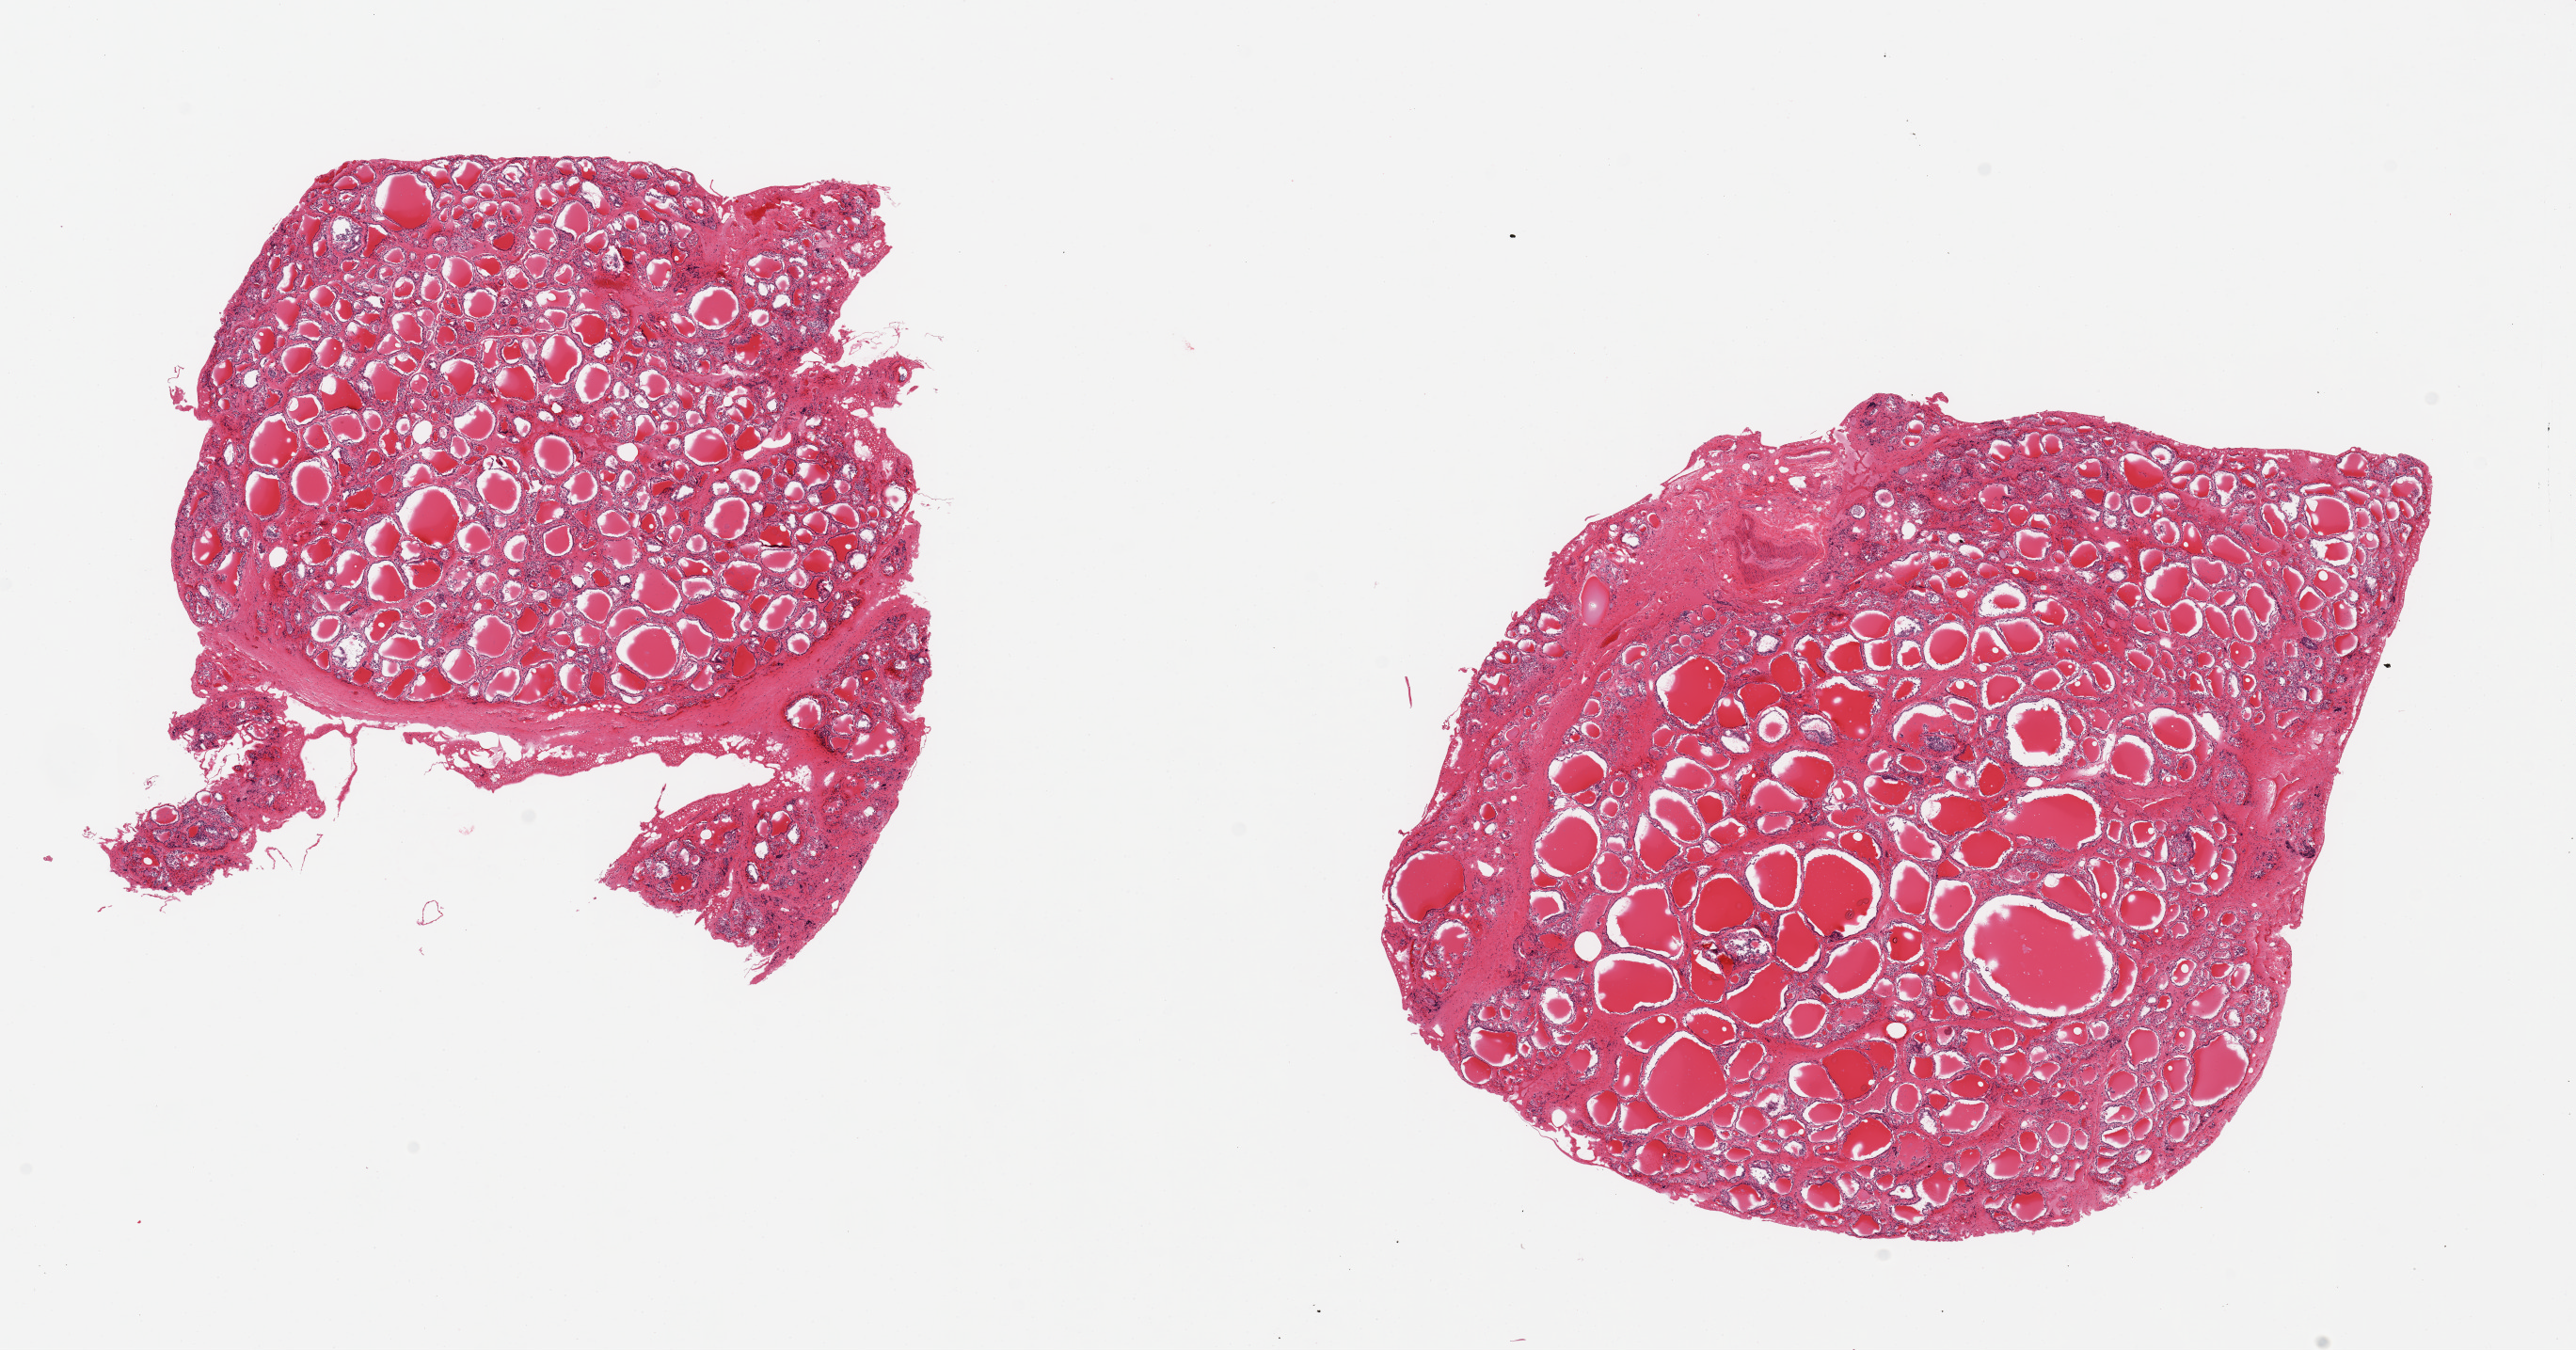
Digitized haematoxylin and eosin-stained section — low-resolution overview of the scanned area, about 21.7 x 11.4 mm. PAXgene-fixed, paraffin-embedded tissue. Section of thyroid (target tissue). Tissue donor sample.
• reviewer comment on this tissue sample: 2 pieces, no abnormalities